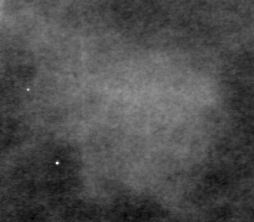
Cropped region of a digitized screen-film mammogram centred on a radiologist-marked abnormality; left breast; CC view.
Marked abnormality: mass, shape irregular, margins ill defined; BI-RADS assessment category 4; pathology result (as recorded, not read from the image): benign.